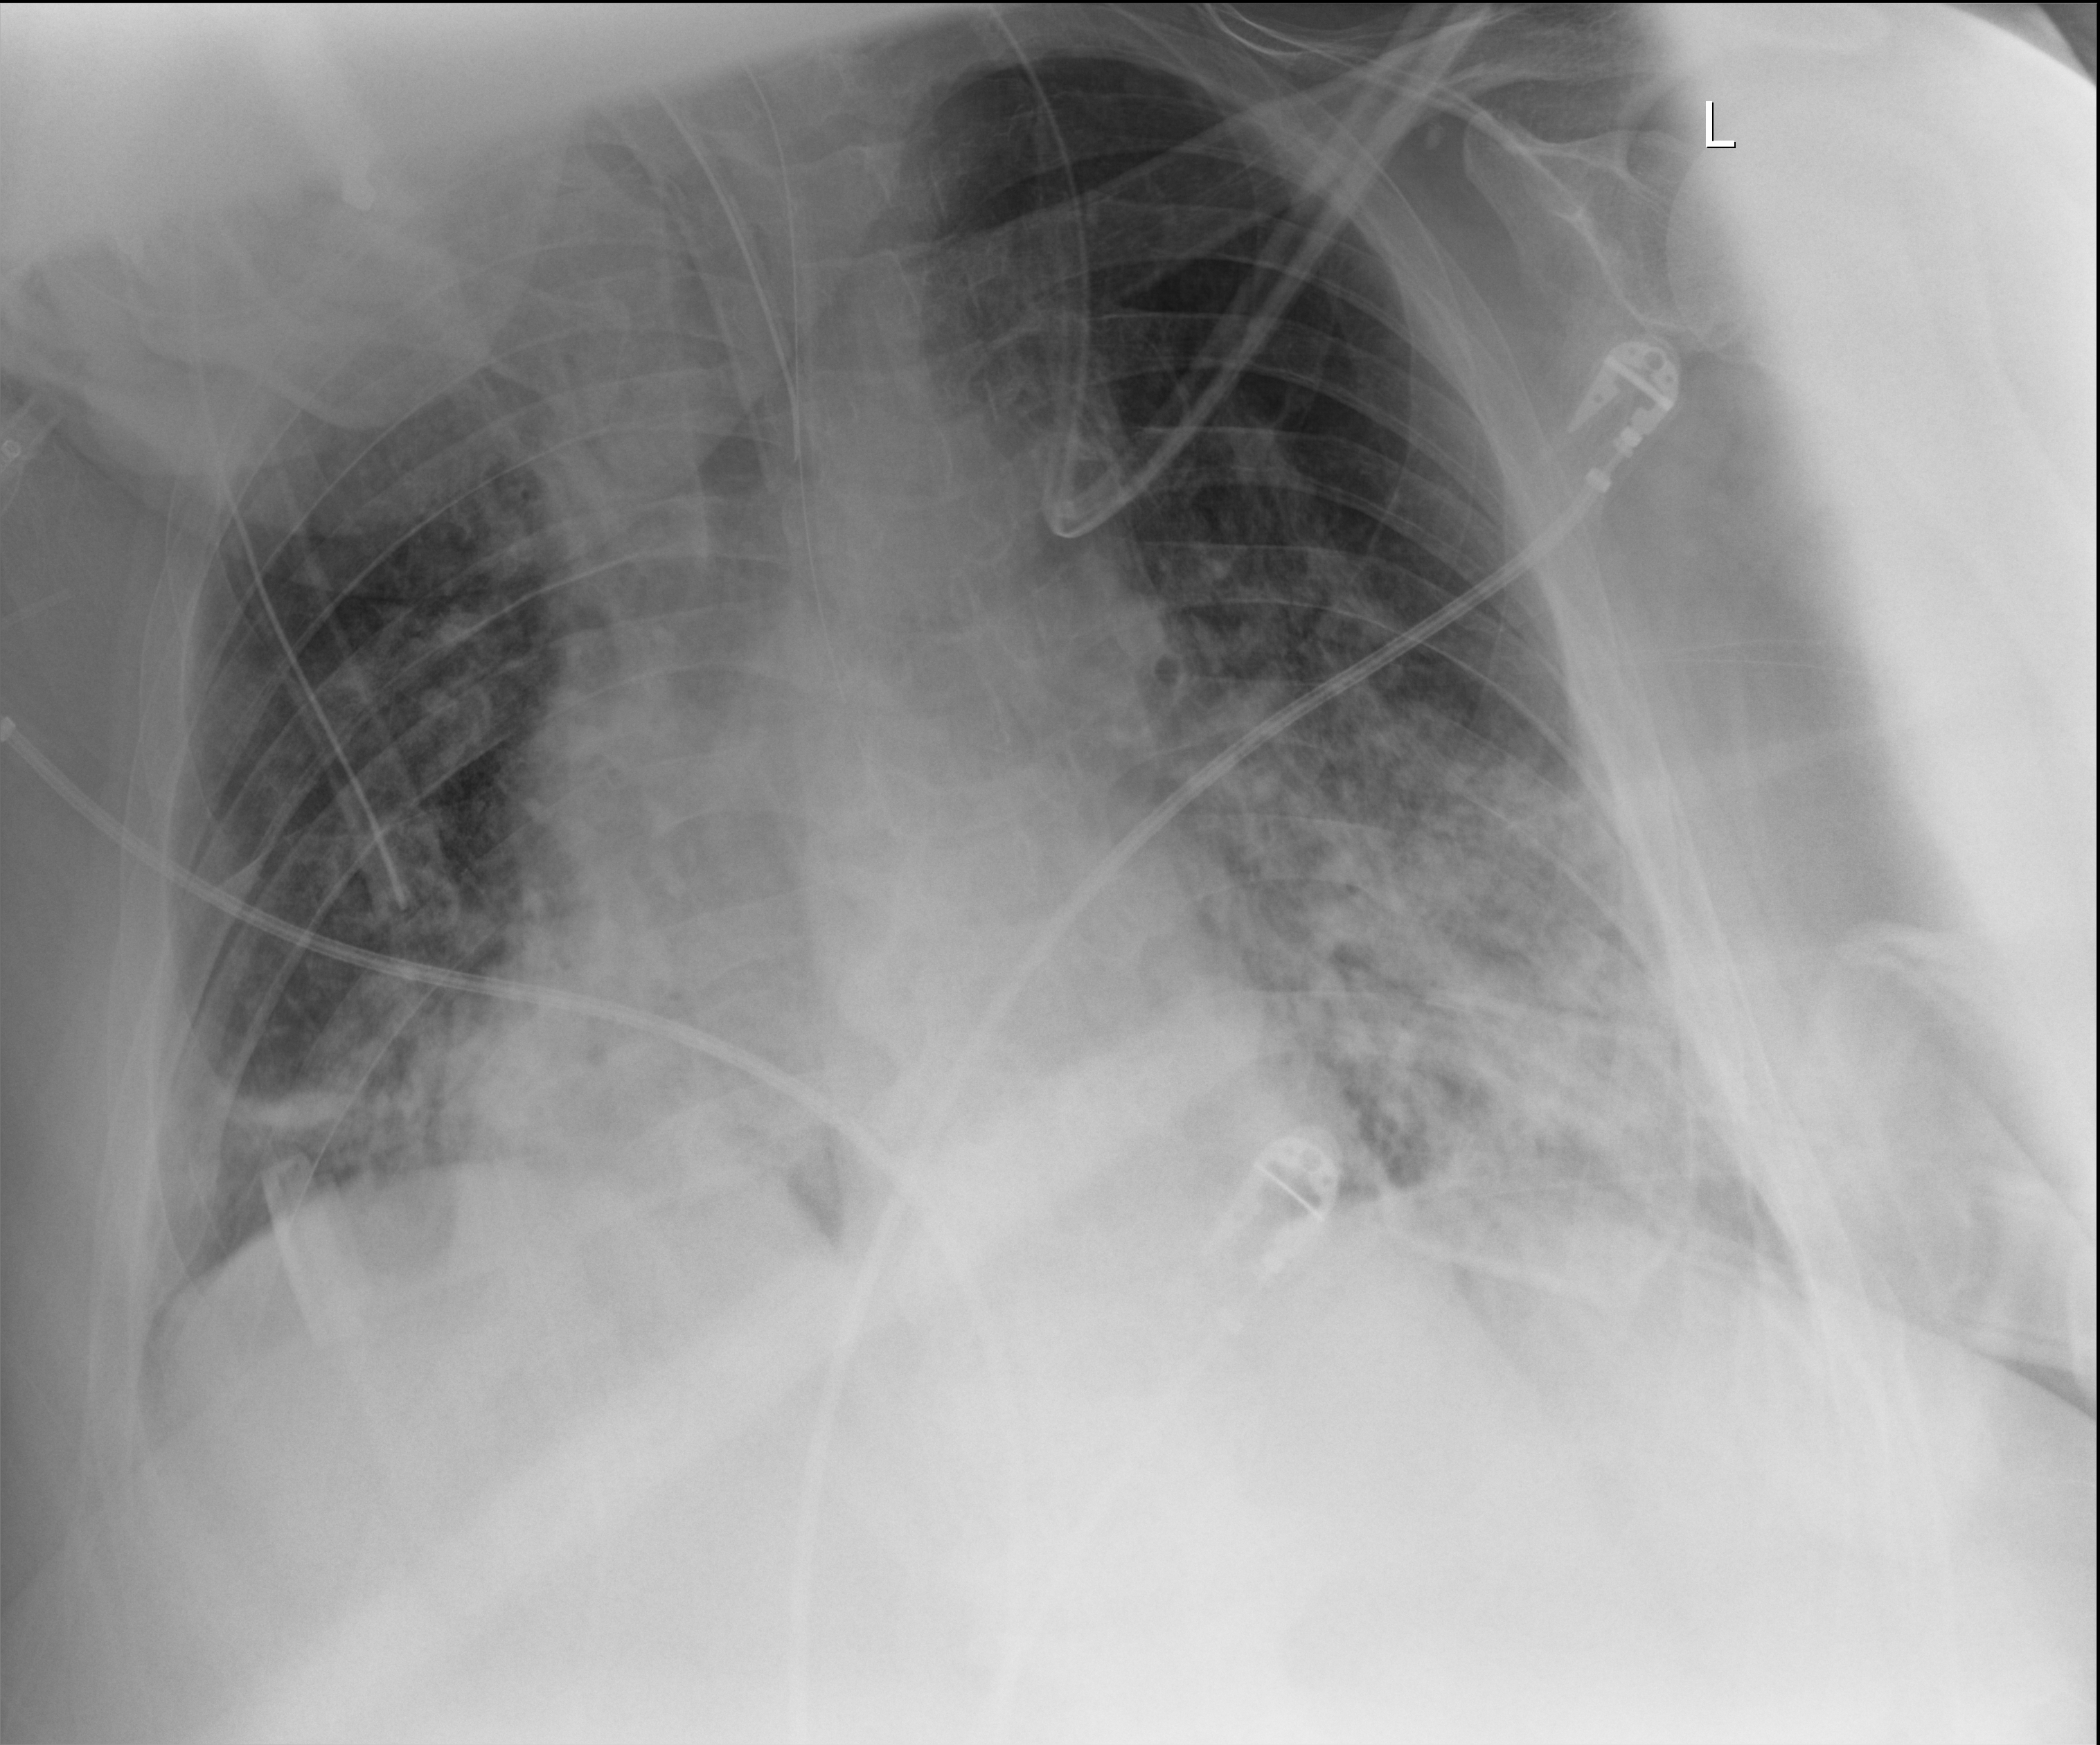
Chest radiograph. Patient hospitalised with COVID-19; male, aged 60–74 years.
Admission-level facts for this patient (not findings on this image; timing relative to this image not recorded): admitted to intensive care during this hospital stay: yes; length of hospital stay: 10 days; mechanically ventilated during this hospital stay: yes.